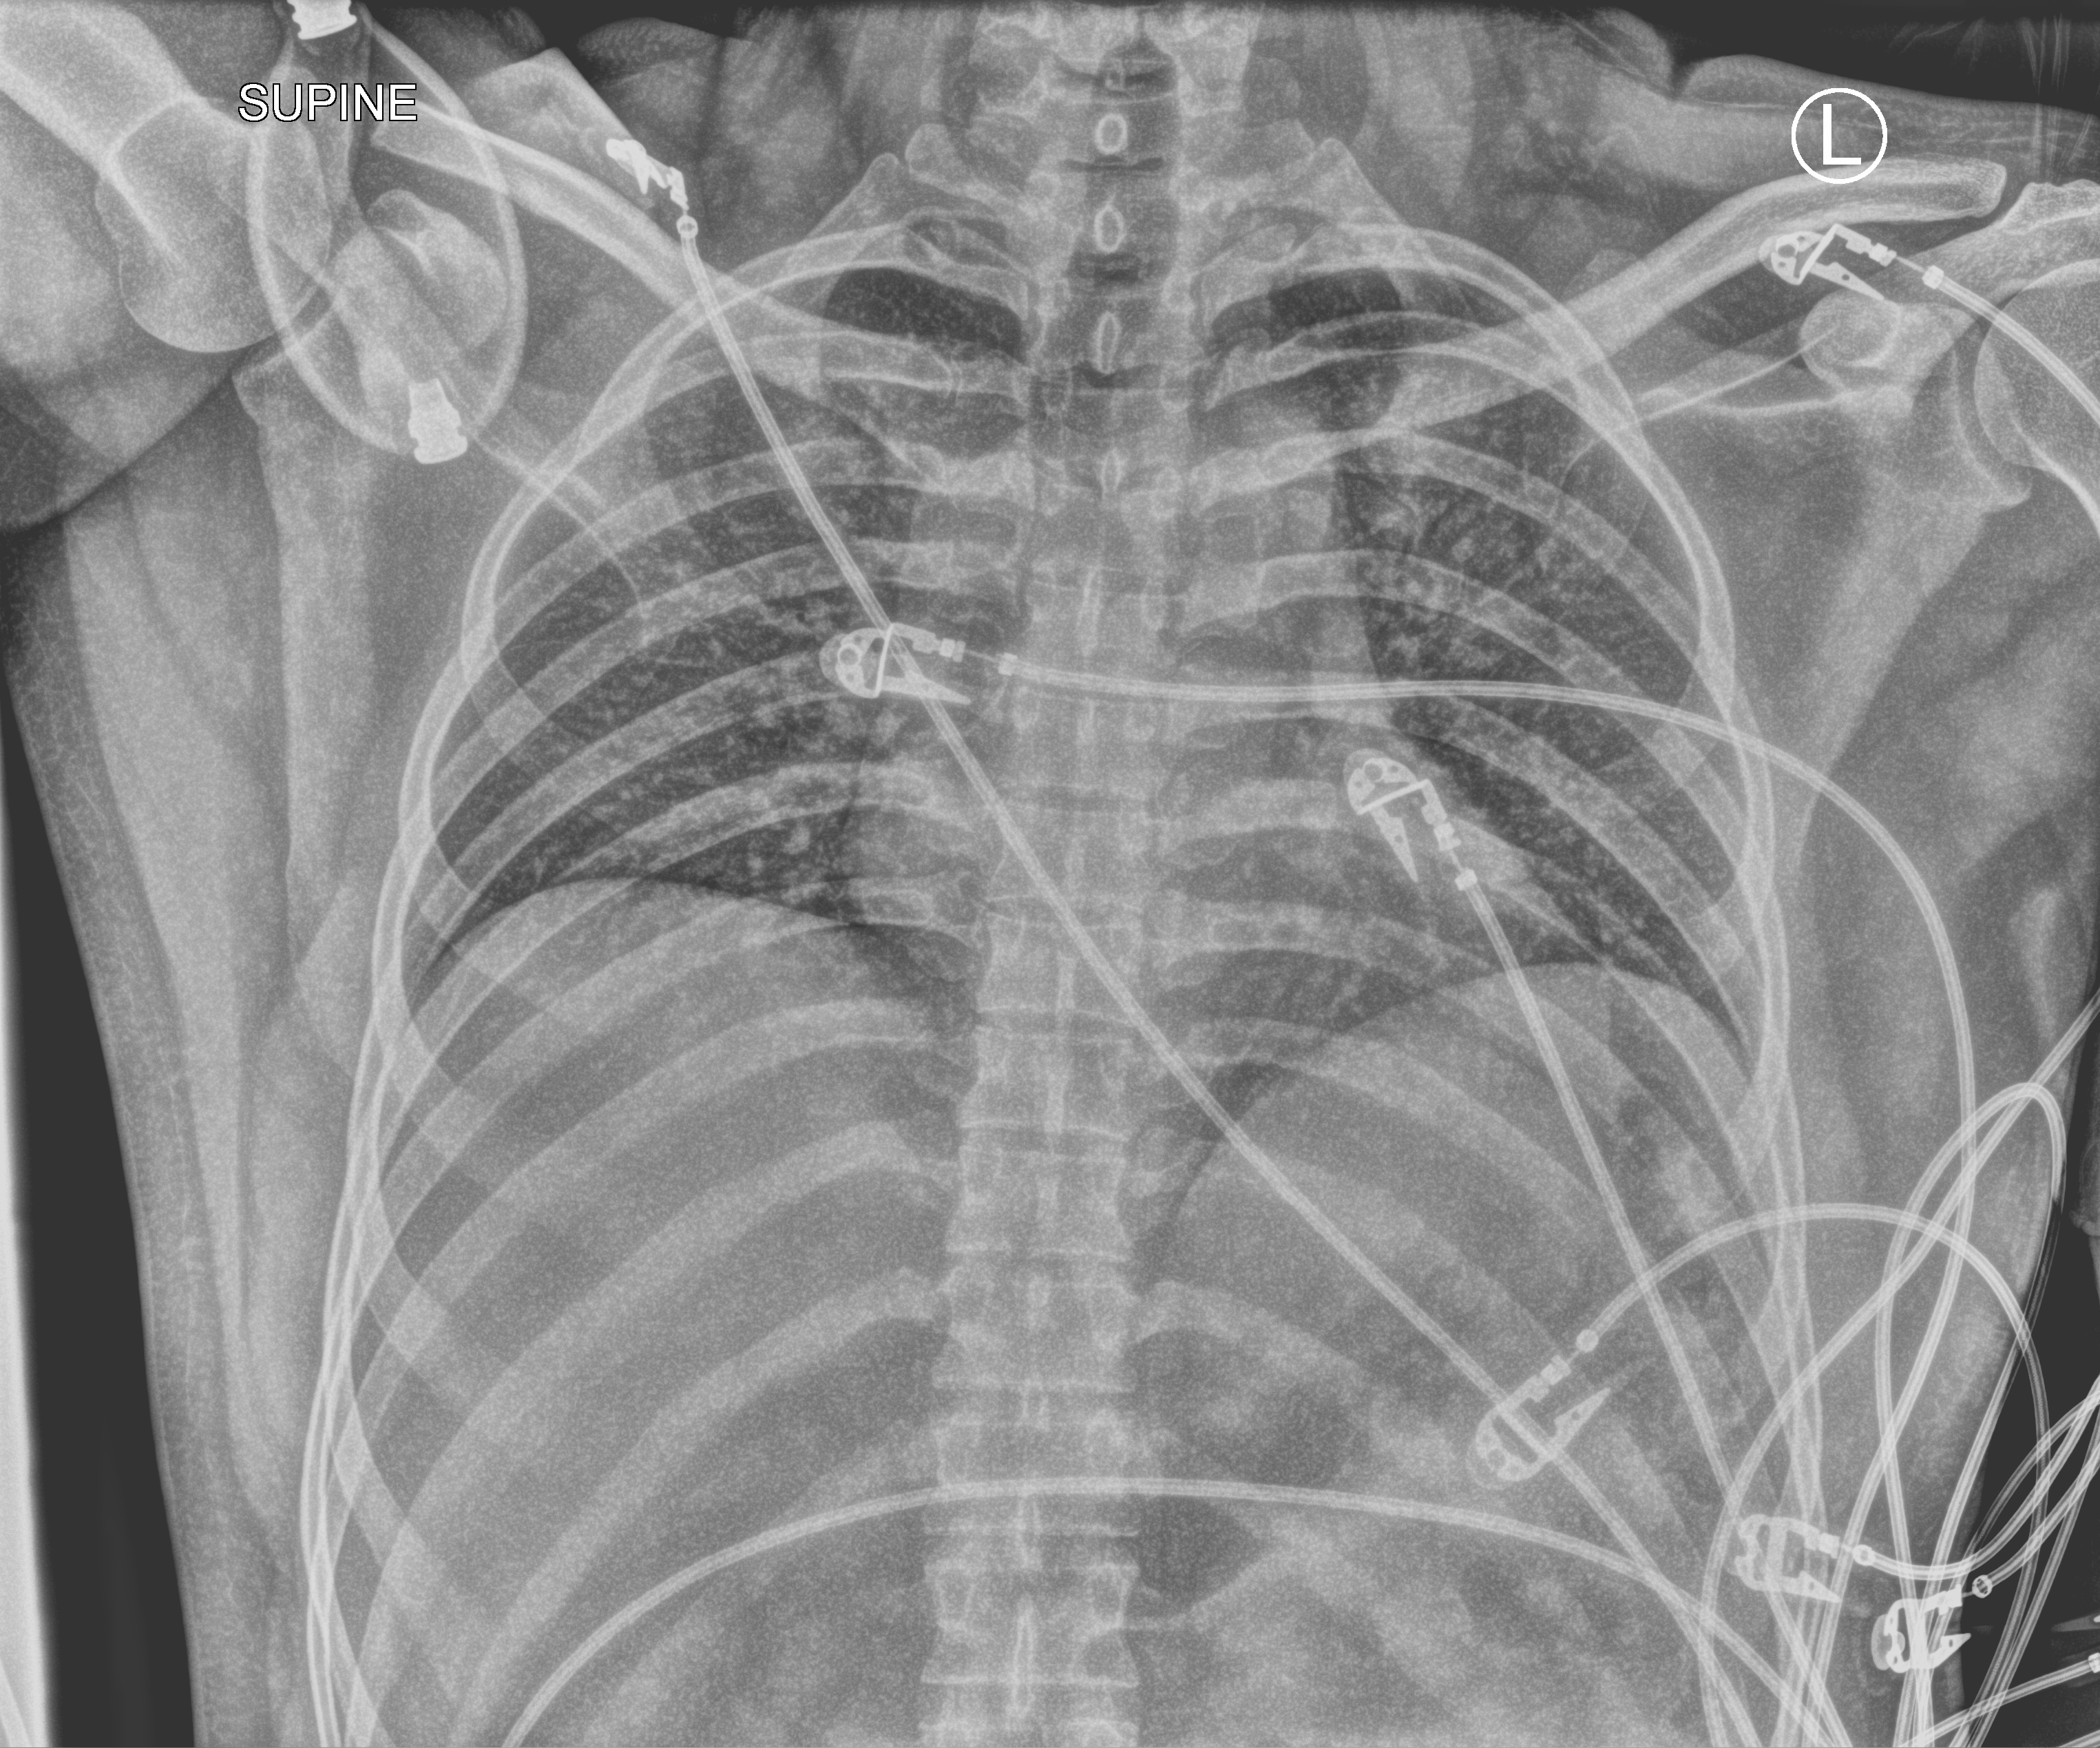
Portable chest radiograph, anteroposterior (AP) projection. Male patient hospitalised with COVID-19, age 18–59 years.
Admission-level facts for this patient (not findings on this image; timing relative to this image not recorded):
- length of hospital stay: 7 days
- mechanically ventilated during this hospital stay: no